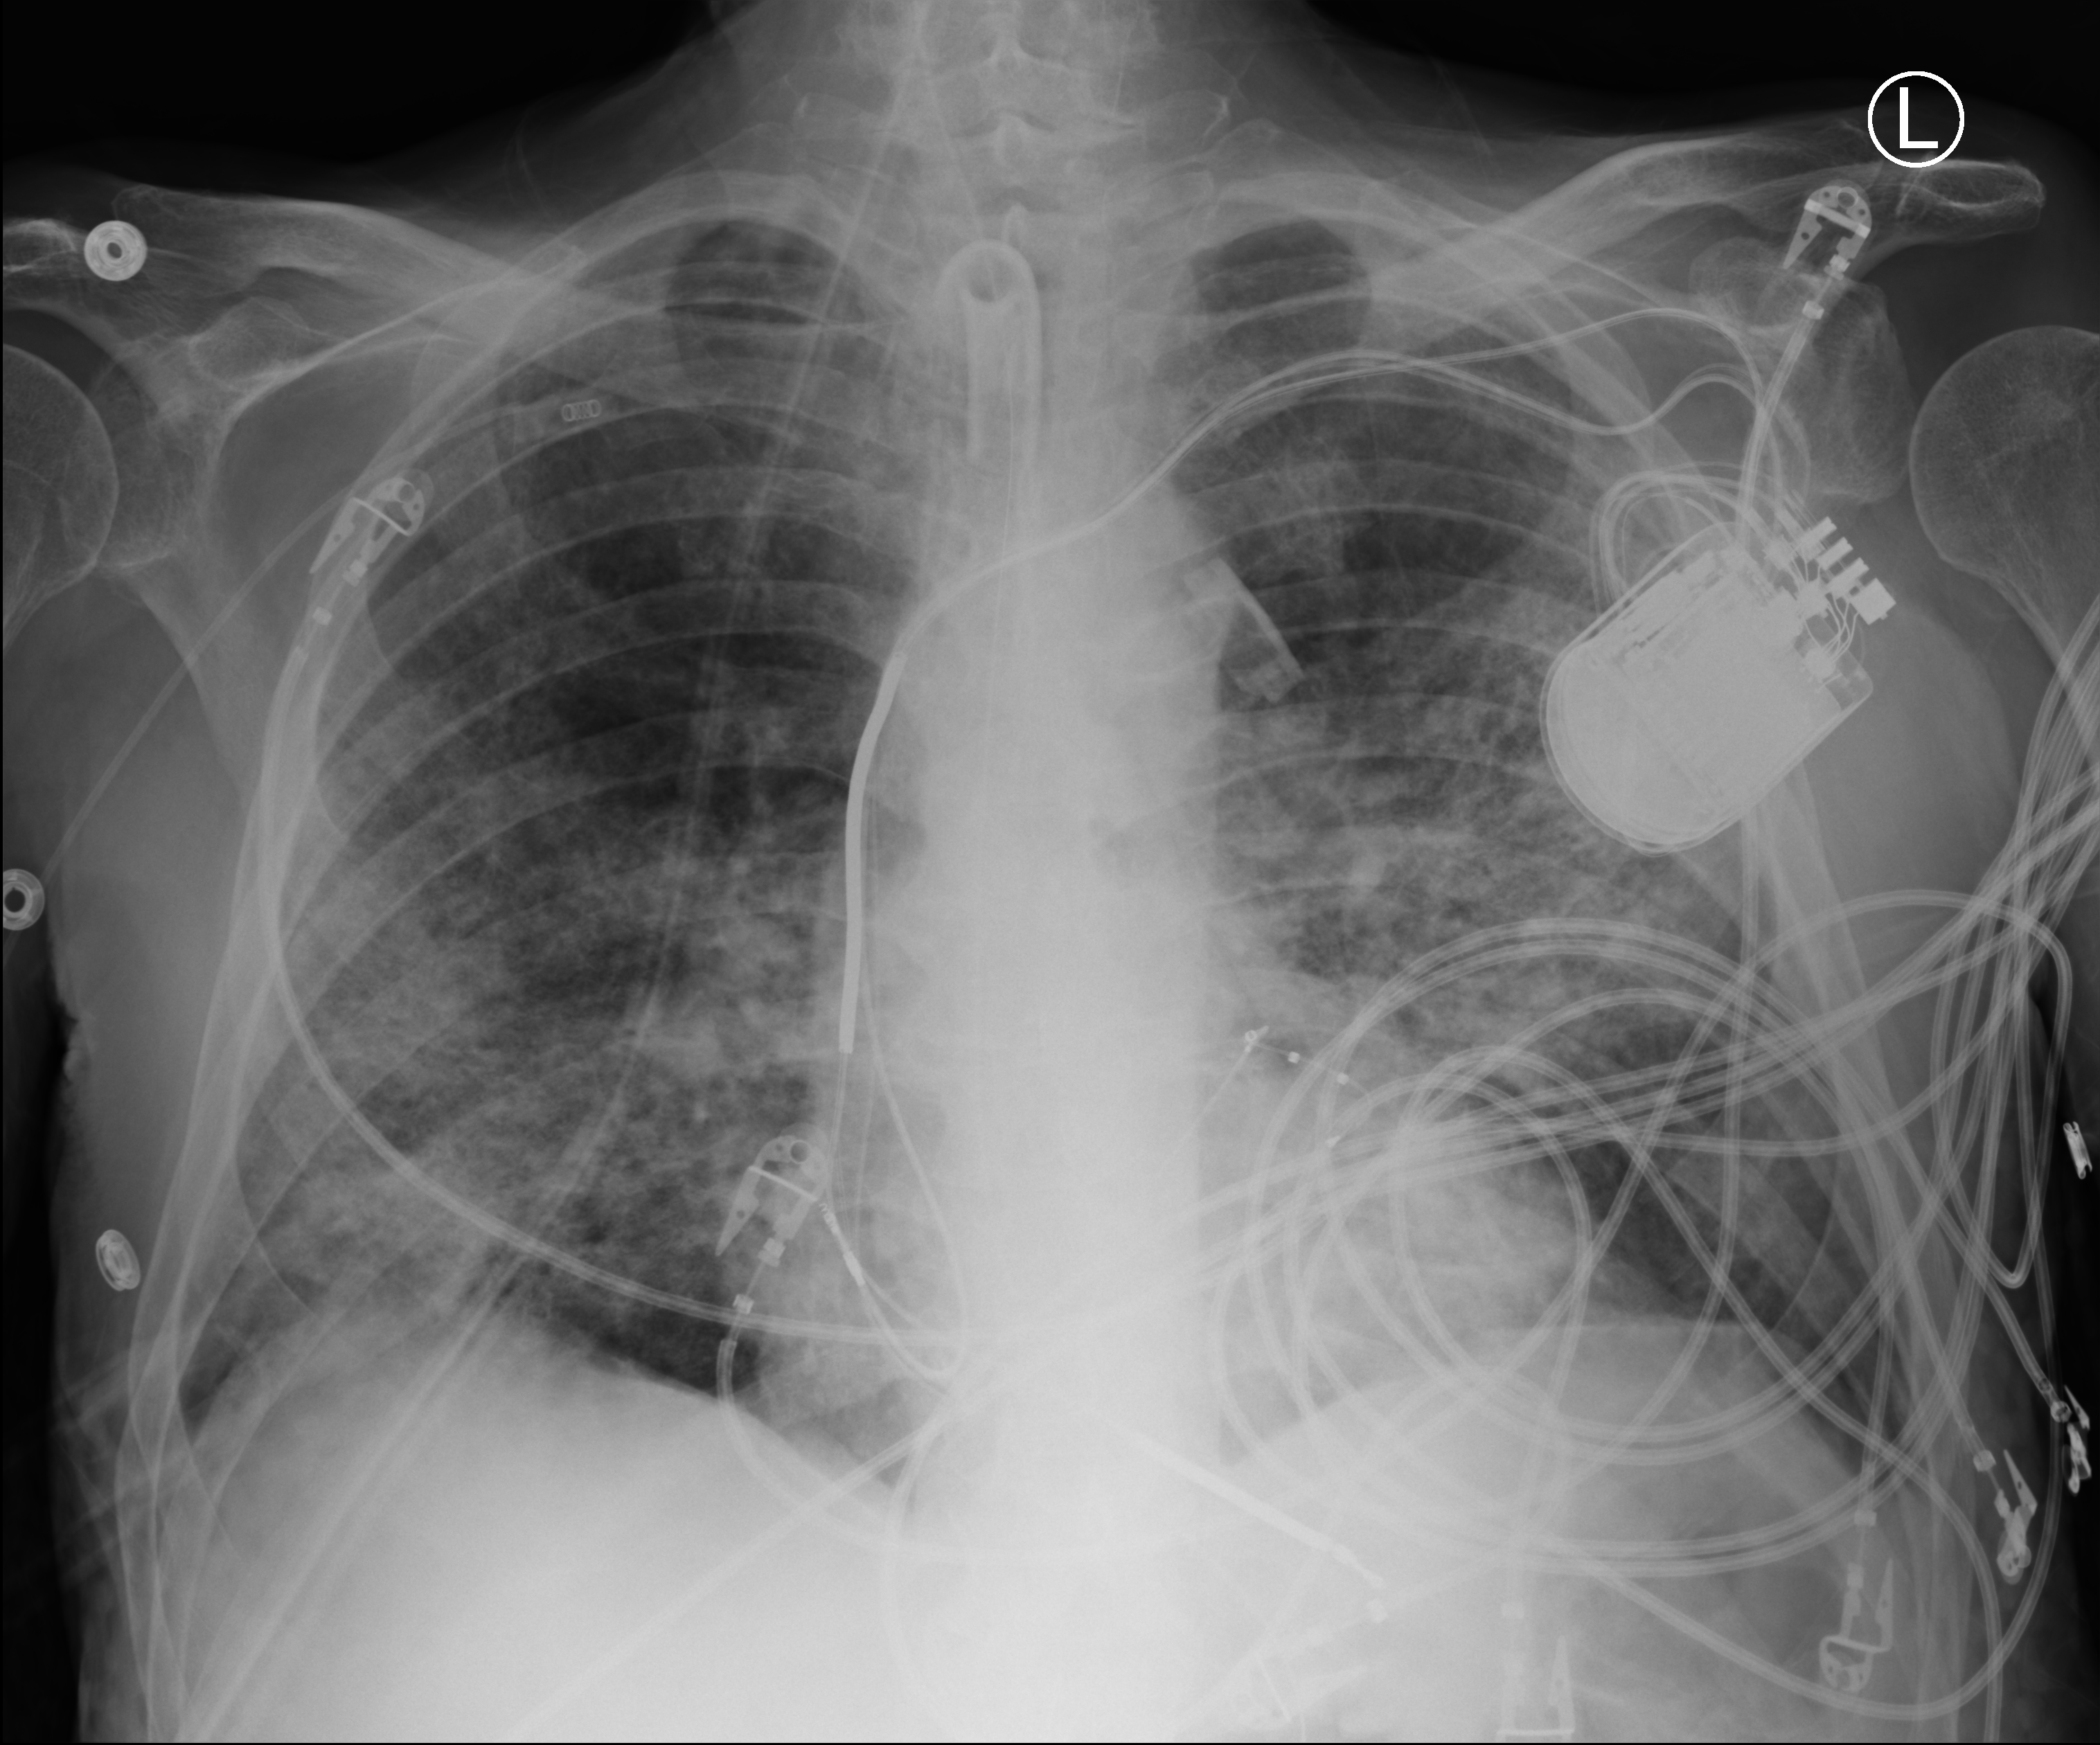
Portable chest radiograph, anteroposterior (AP) projection. Male patient hospitalised with COVID-19, age 60–74 years.
From the hospital-stay record, not from the radiograph (when in the stay this image was taken is not recorded): mechanically ventilated during this hospital stay: yes.